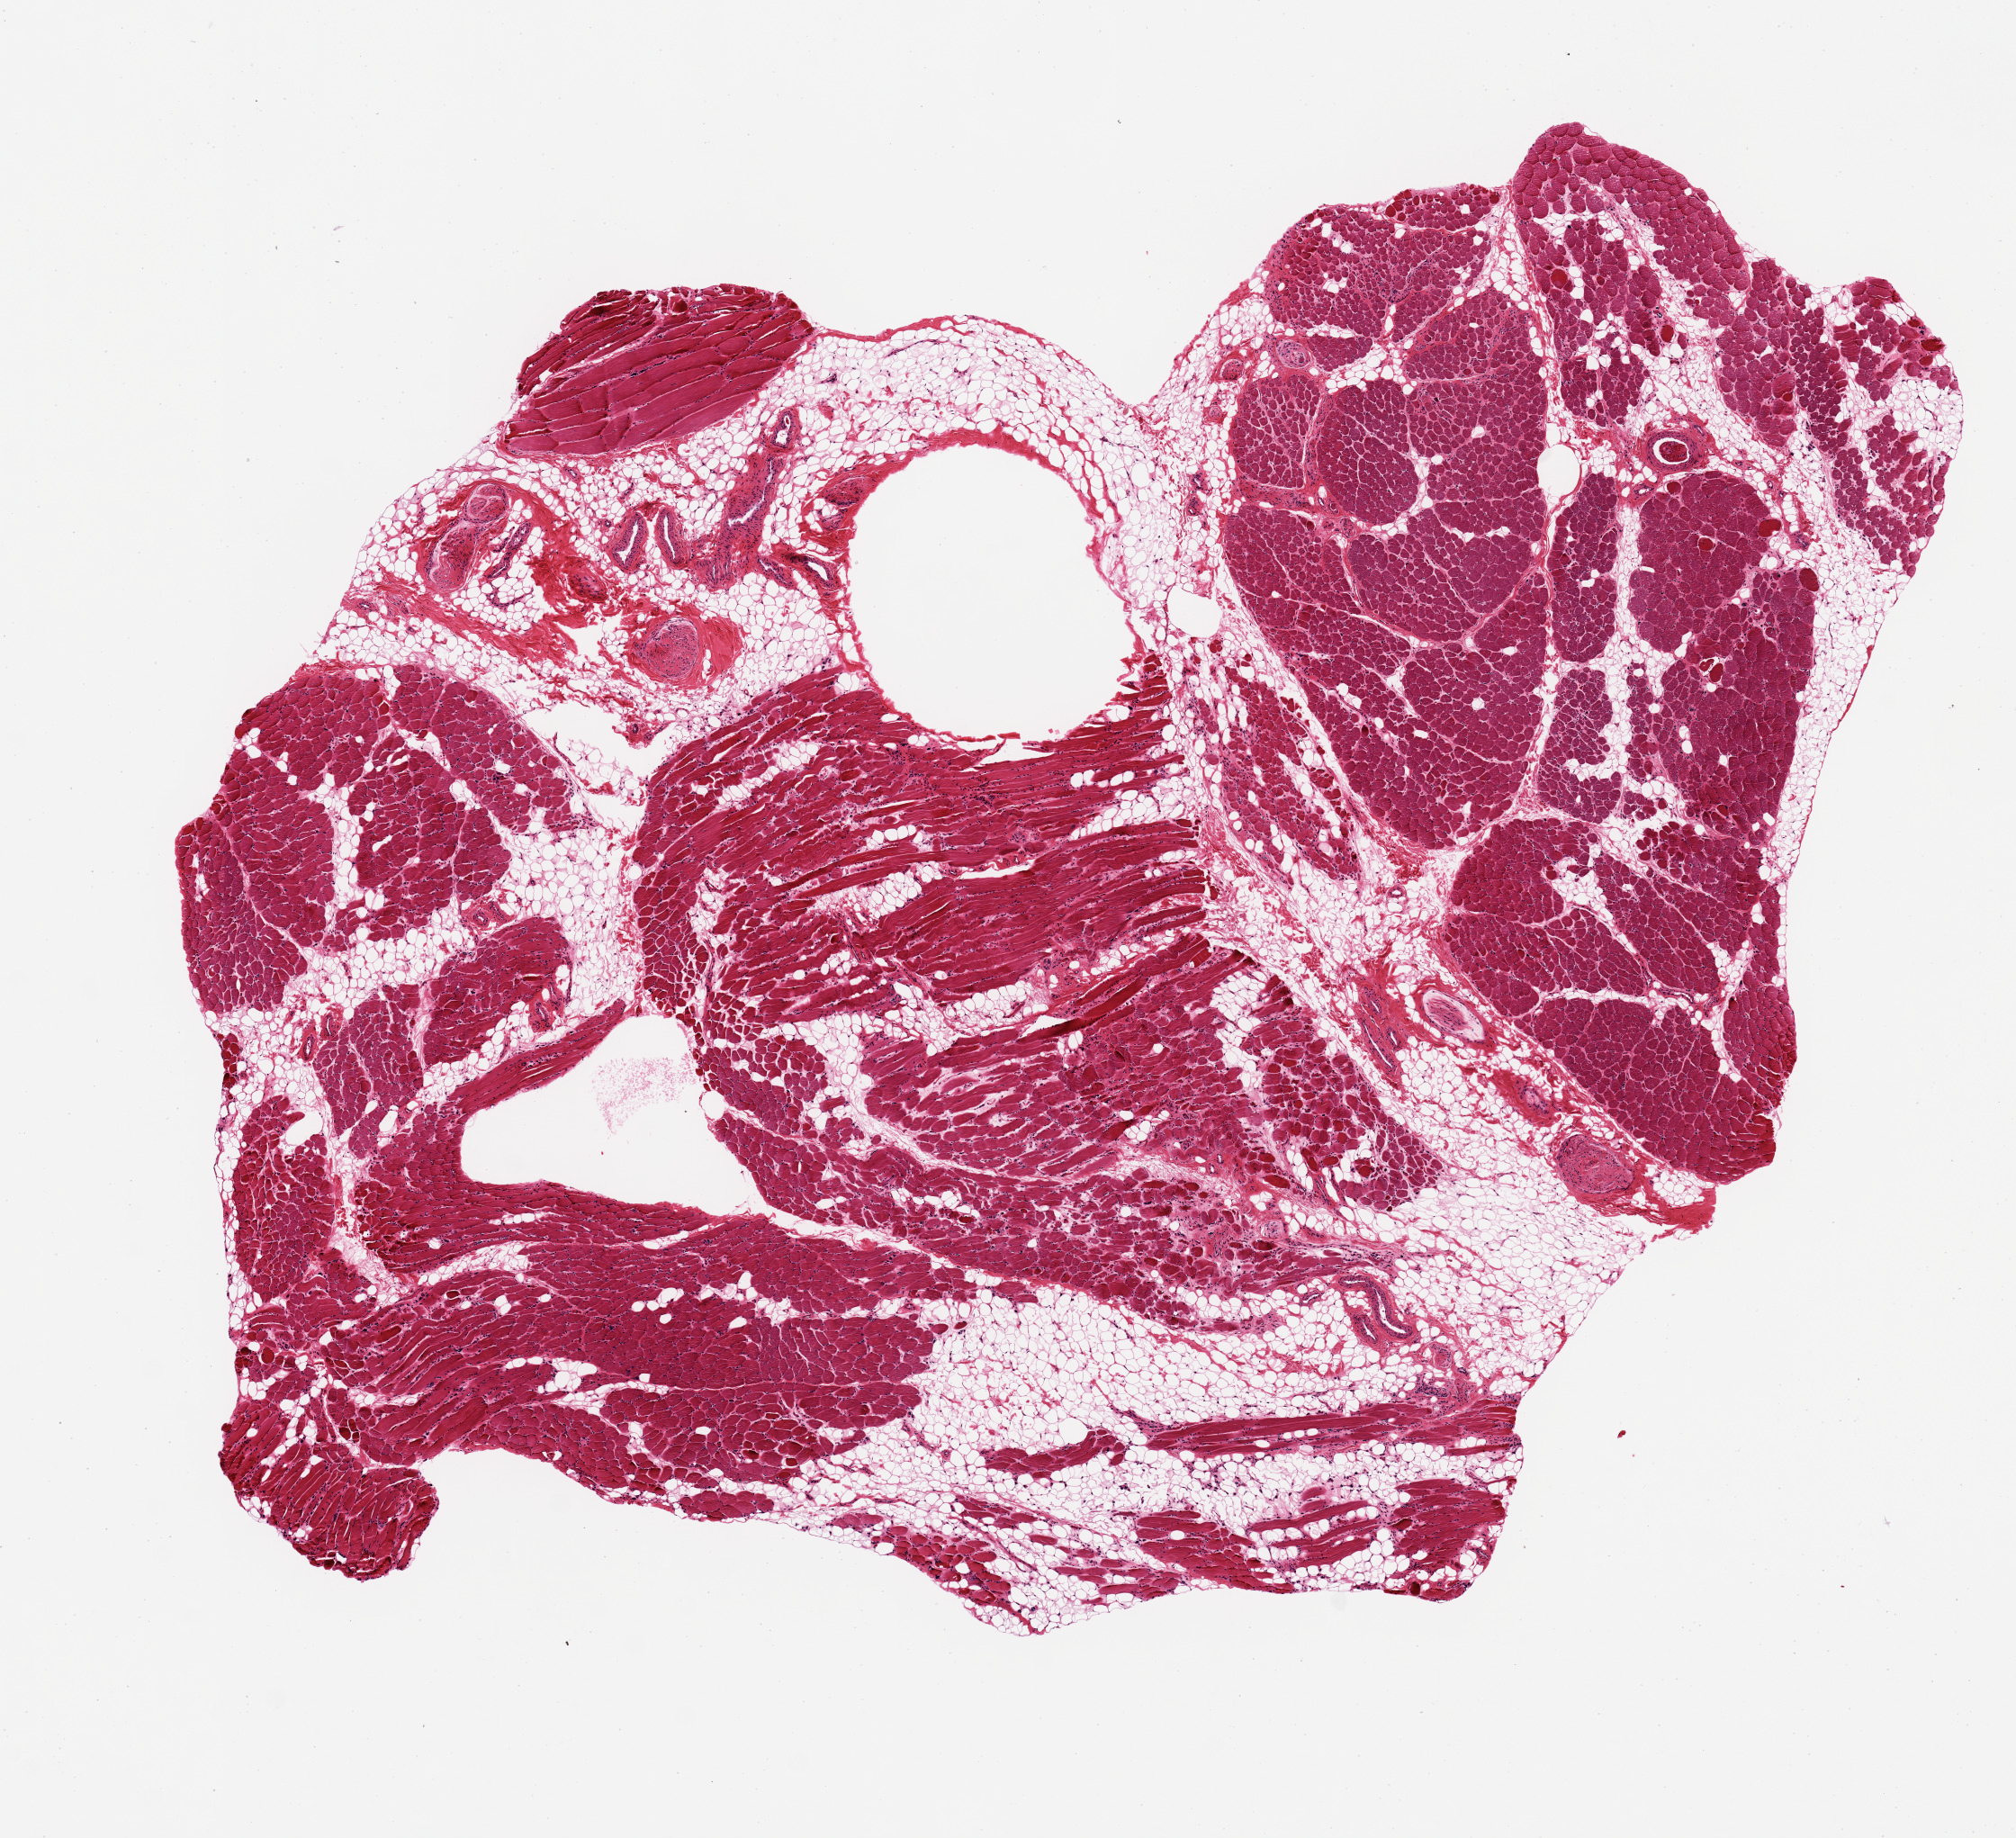
H&E whole-slide image, brightfield — low-resolution overview of the scanned area, about 8.9 x 8.1 mm. PAXgene-fixed, paraffin-embedded tissue. Sampled site (target tissue): skeletal muscle. Donor tissue sample. Donor: male.
Reviewer comment on this tissue sample: 8.6x6.8mm ~50% intermingled adipose tissue.